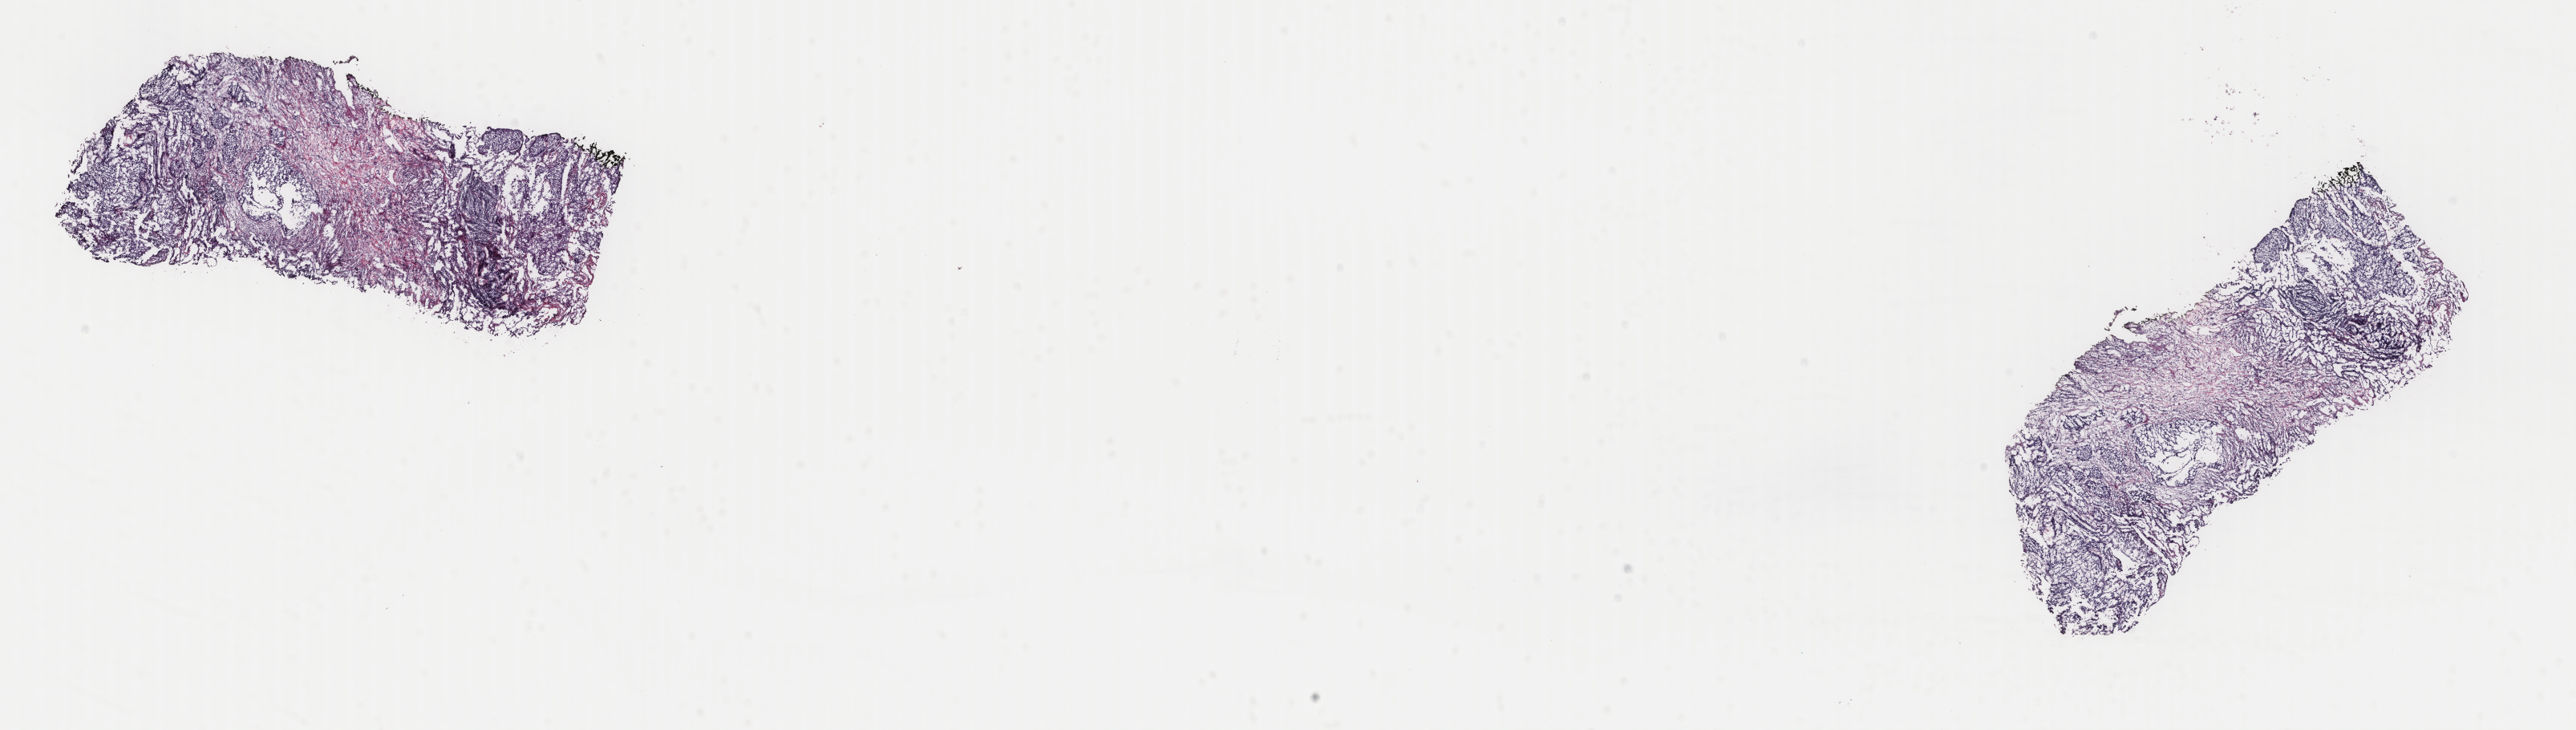
Digitized H&E tissue section (whole slide) — low-resolution overview of the scanned area, about 25.5 x 7.2 mm; frozen section from the top of the tissue portion; lung, primary tumour sample. Male, age 66 years at initial diagnosis. Pathologist review of this section (percent, as recorded): tumour cells 50%, tumour nuclei 60%, normal cells 5%, stromal cells 35%, necrosis 10%. Inflammatory infiltration, as recorded: lymphocyte infiltration 0%, monocyte infiltration 0%, neutrophil infiltration 0%.
- histologic diagnosis: Squamous cell carcinoma, NOS (upper lobe, lung)
- AJCC pathologic stage: IIIA (6th edition)